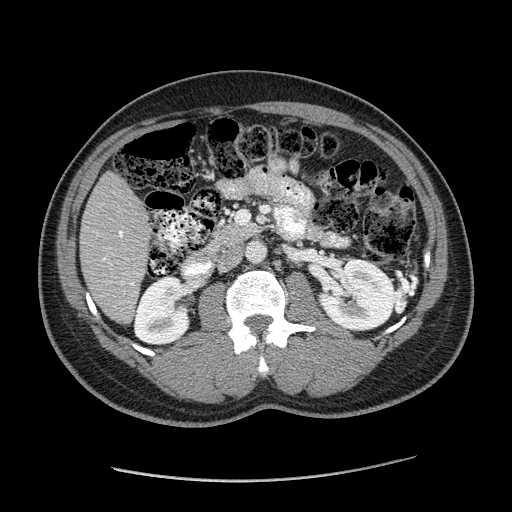
Contrast-enhanced abdominal CT (liver protocol), one axial slice. Position 61 of 182 along the scan axis. Reconstruction kernel STANDARD. Soft-tissue window (W 400 / L 40 HU). 512 × 512 image matrix. From the clinical record (not read from this slice): diagnosis: hepatocellular carcinoma (patient treated with transarterial chemoembolisation; whether this scan precedes or follows treatment is not stated here); TNM stage (as recorded): Stage-I; Child-Pugh class: A; tumour differentiation: well differentiated; tumour nodularity: uninodular.
Outlined on this slice (semi-automatically segmented with operator editing):
- liver parenchyma outside the tumour (the mass and vessels are separate outlines, so this box may not span the whole liver): bounding box [x1, y1, x2, y2] px = [80, 172, 150, 322]
- liver vessels: [103, 231, 134, 286]